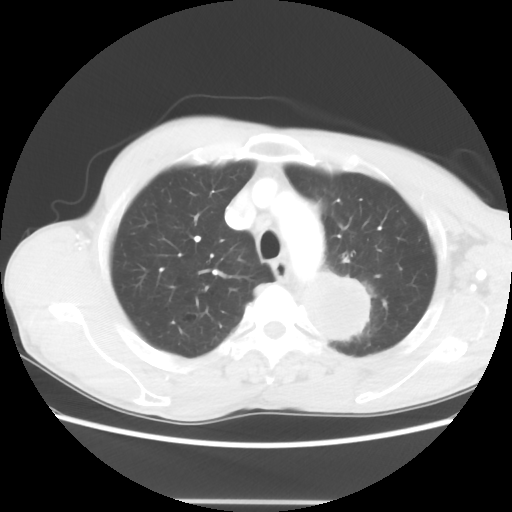
Chest CT, one axial slice. Position 51 of 62 along the scan axis. 100 kVp. Lung window (W 1500 / L -600 HU). 5 mm slice thickness. 512 × 512 image matrix, field of view 360 × 360 mm. Patient: male, 61 years. From the clinical record (not read from this slice): clinical TNM (as recorded): T3 N1 M1.
Outlined on this slice (rectangle marked by the reading radiologist):
- lung tumour (recorded histology: adenocarcinoma): bounding box <301,271,375,345> (left, top, right, bottom; pixels)